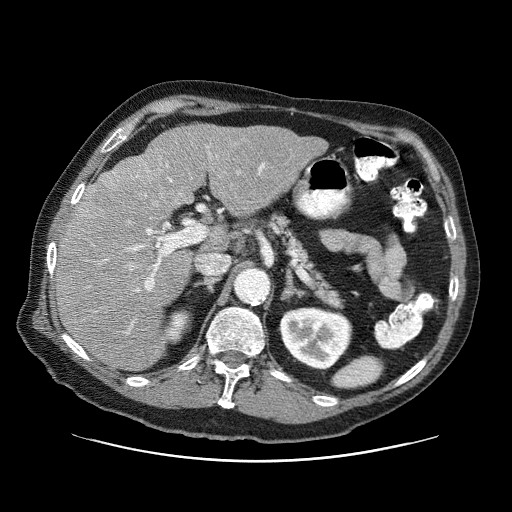
Contrast-enhanced abdominal CT (liver protocol), one axial slice; slice 42 of 87 in the series (ordered by position); 120 kVp; one of 3 acquisitions stored at this slice position; soft-tissue window (W 400 / L 40 HU); 2.5 mm slice thickness; 512 × 512 image matrix. From the clinical record (not read from this slice): diagnosis: hepatocellular carcinoma (patient treated with transarterial chemoembolisation; whether this scan precedes or follows treatment is not stated here); TNM stage (as recorded): Stage-IIIA.
Annotated regions visible in this slice (semi-automatically segmented with operator editing):
- liver parenchyma outside the tumour (the mass and vessels are separate outlines, so this box may not span the whole liver): bounding box [x1, y1, x2, y2] px = [56, 124, 328, 370]
- mass: [104, 158, 148, 206]
- liver vessels: [81, 146, 265, 324]